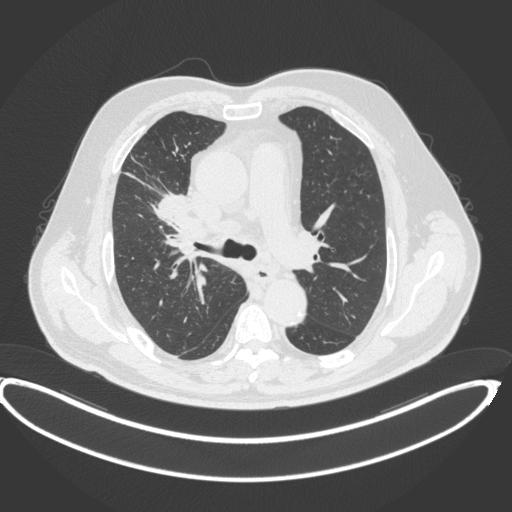
Chest CT, one axial slice; slice 266 of 395 in the series (ordered by position); 120 kVp; lung window (W 1500 / L -600 HU); 1 mm slice thickness; 512 × 512 image matrix, field of view 448 × 448 mm. Male patient, age 62 years. From the clinical record (not read from this slice): clinical TNM (as recorded): T1c N3 M1c.
Structures marked on this image (rectangle marked by the reading radiologist):
- lung tumour (recorded histology: adenocarcinoma): bounding box [x1, y1, x2, y2] px = [147, 184, 192, 228]